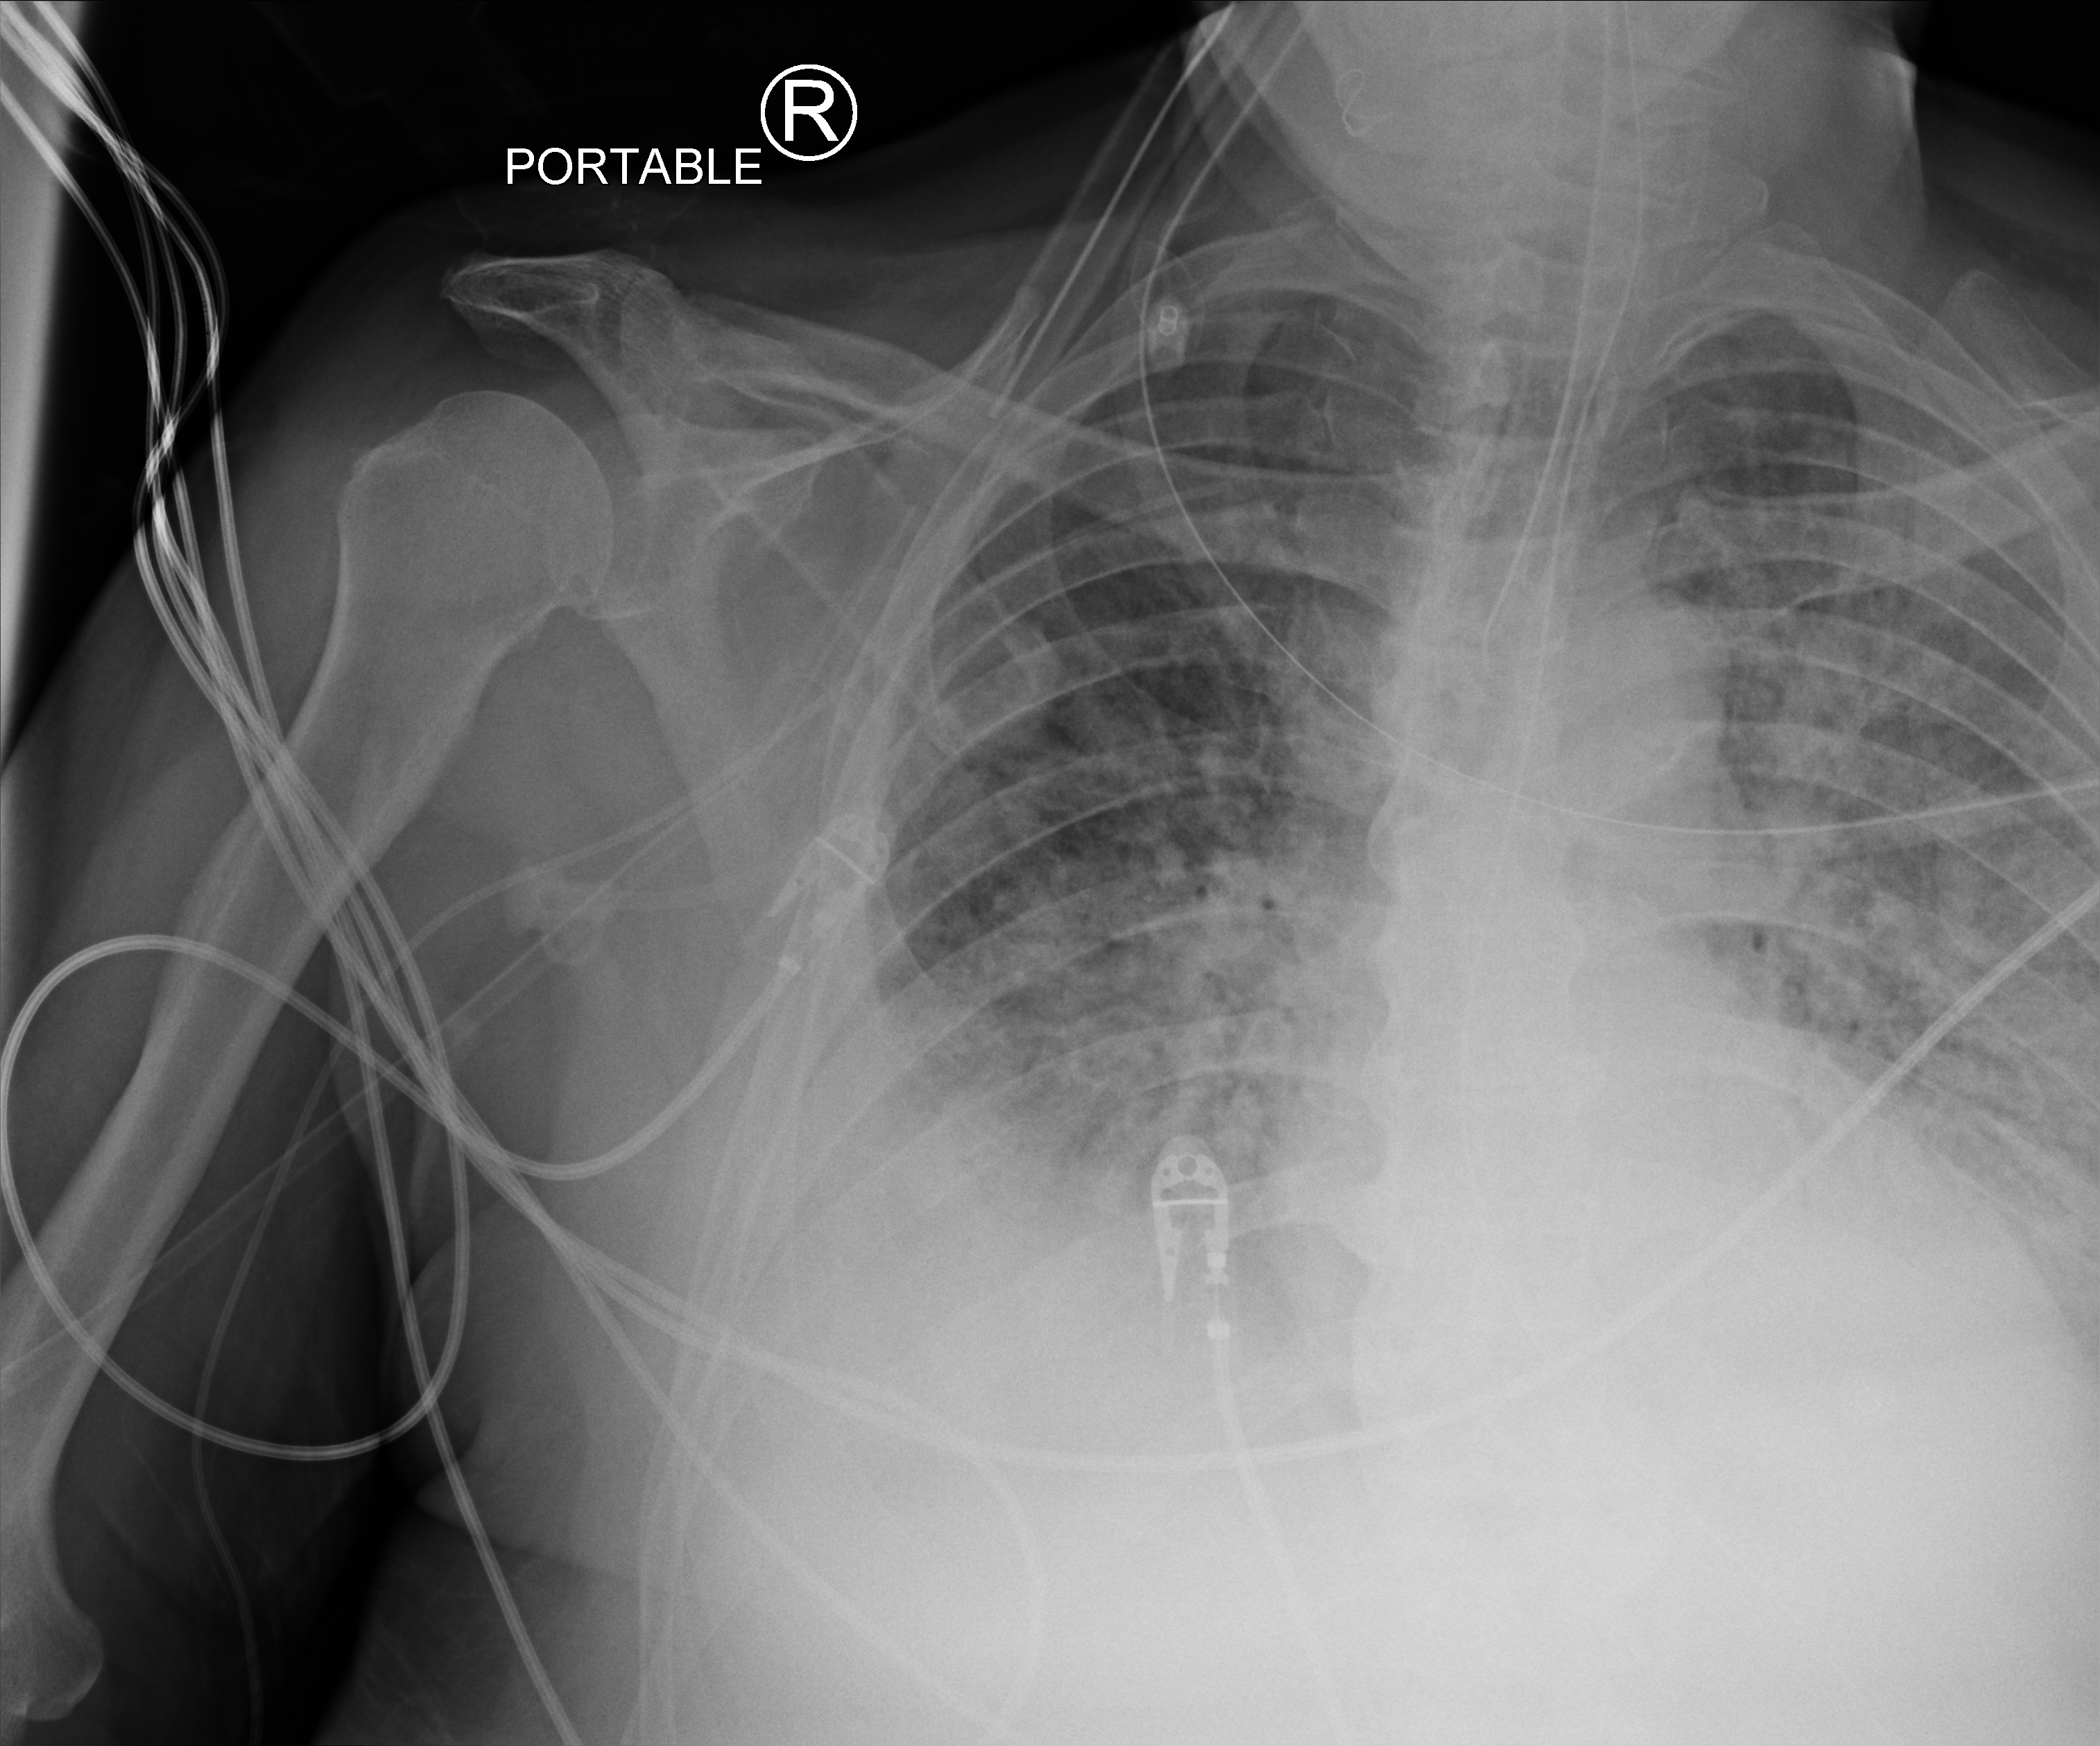
Chest X-ray (portable), anteroposterior (AP) projection. Patient hospitalised with COVID-19; male, aged 60–74 years.
Hospital-stay facts (about this admission, not read from this image; timing relative to this image not recorded): mechanically ventilated during this hospital stay: yes.